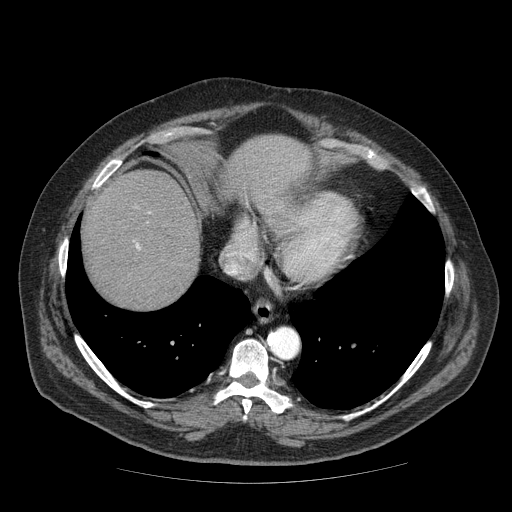
Contrast-enhanced abdominal CT (liver protocol), one axial slice; position 63 of 85 along the scan axis; 120 kVp; soft-tissue window (W 400 / L 40 HU); 512 × 512 image matrix. From the clinical record (not read from this slice): diagnosis: hepatocellular carcinoma (patient treated with transarterial chemoembolisation; whether this scan precedes or follows treatment is not stated here); TNM stage (as recorded): Stage-IIIA; Child-Pugh class: A; tumour nodularity: multinodular.
Structures marked on this image (semi-automatically segmented with operator editing):
- liver parenchyma outside the tumour (the mass and vessels are separate outlines, so this box may not span the whole liver): box from (x=82, y=136) to (x=308, y=308) px
- liver vessels: (x=136, y=244)–(x=140, y=249)